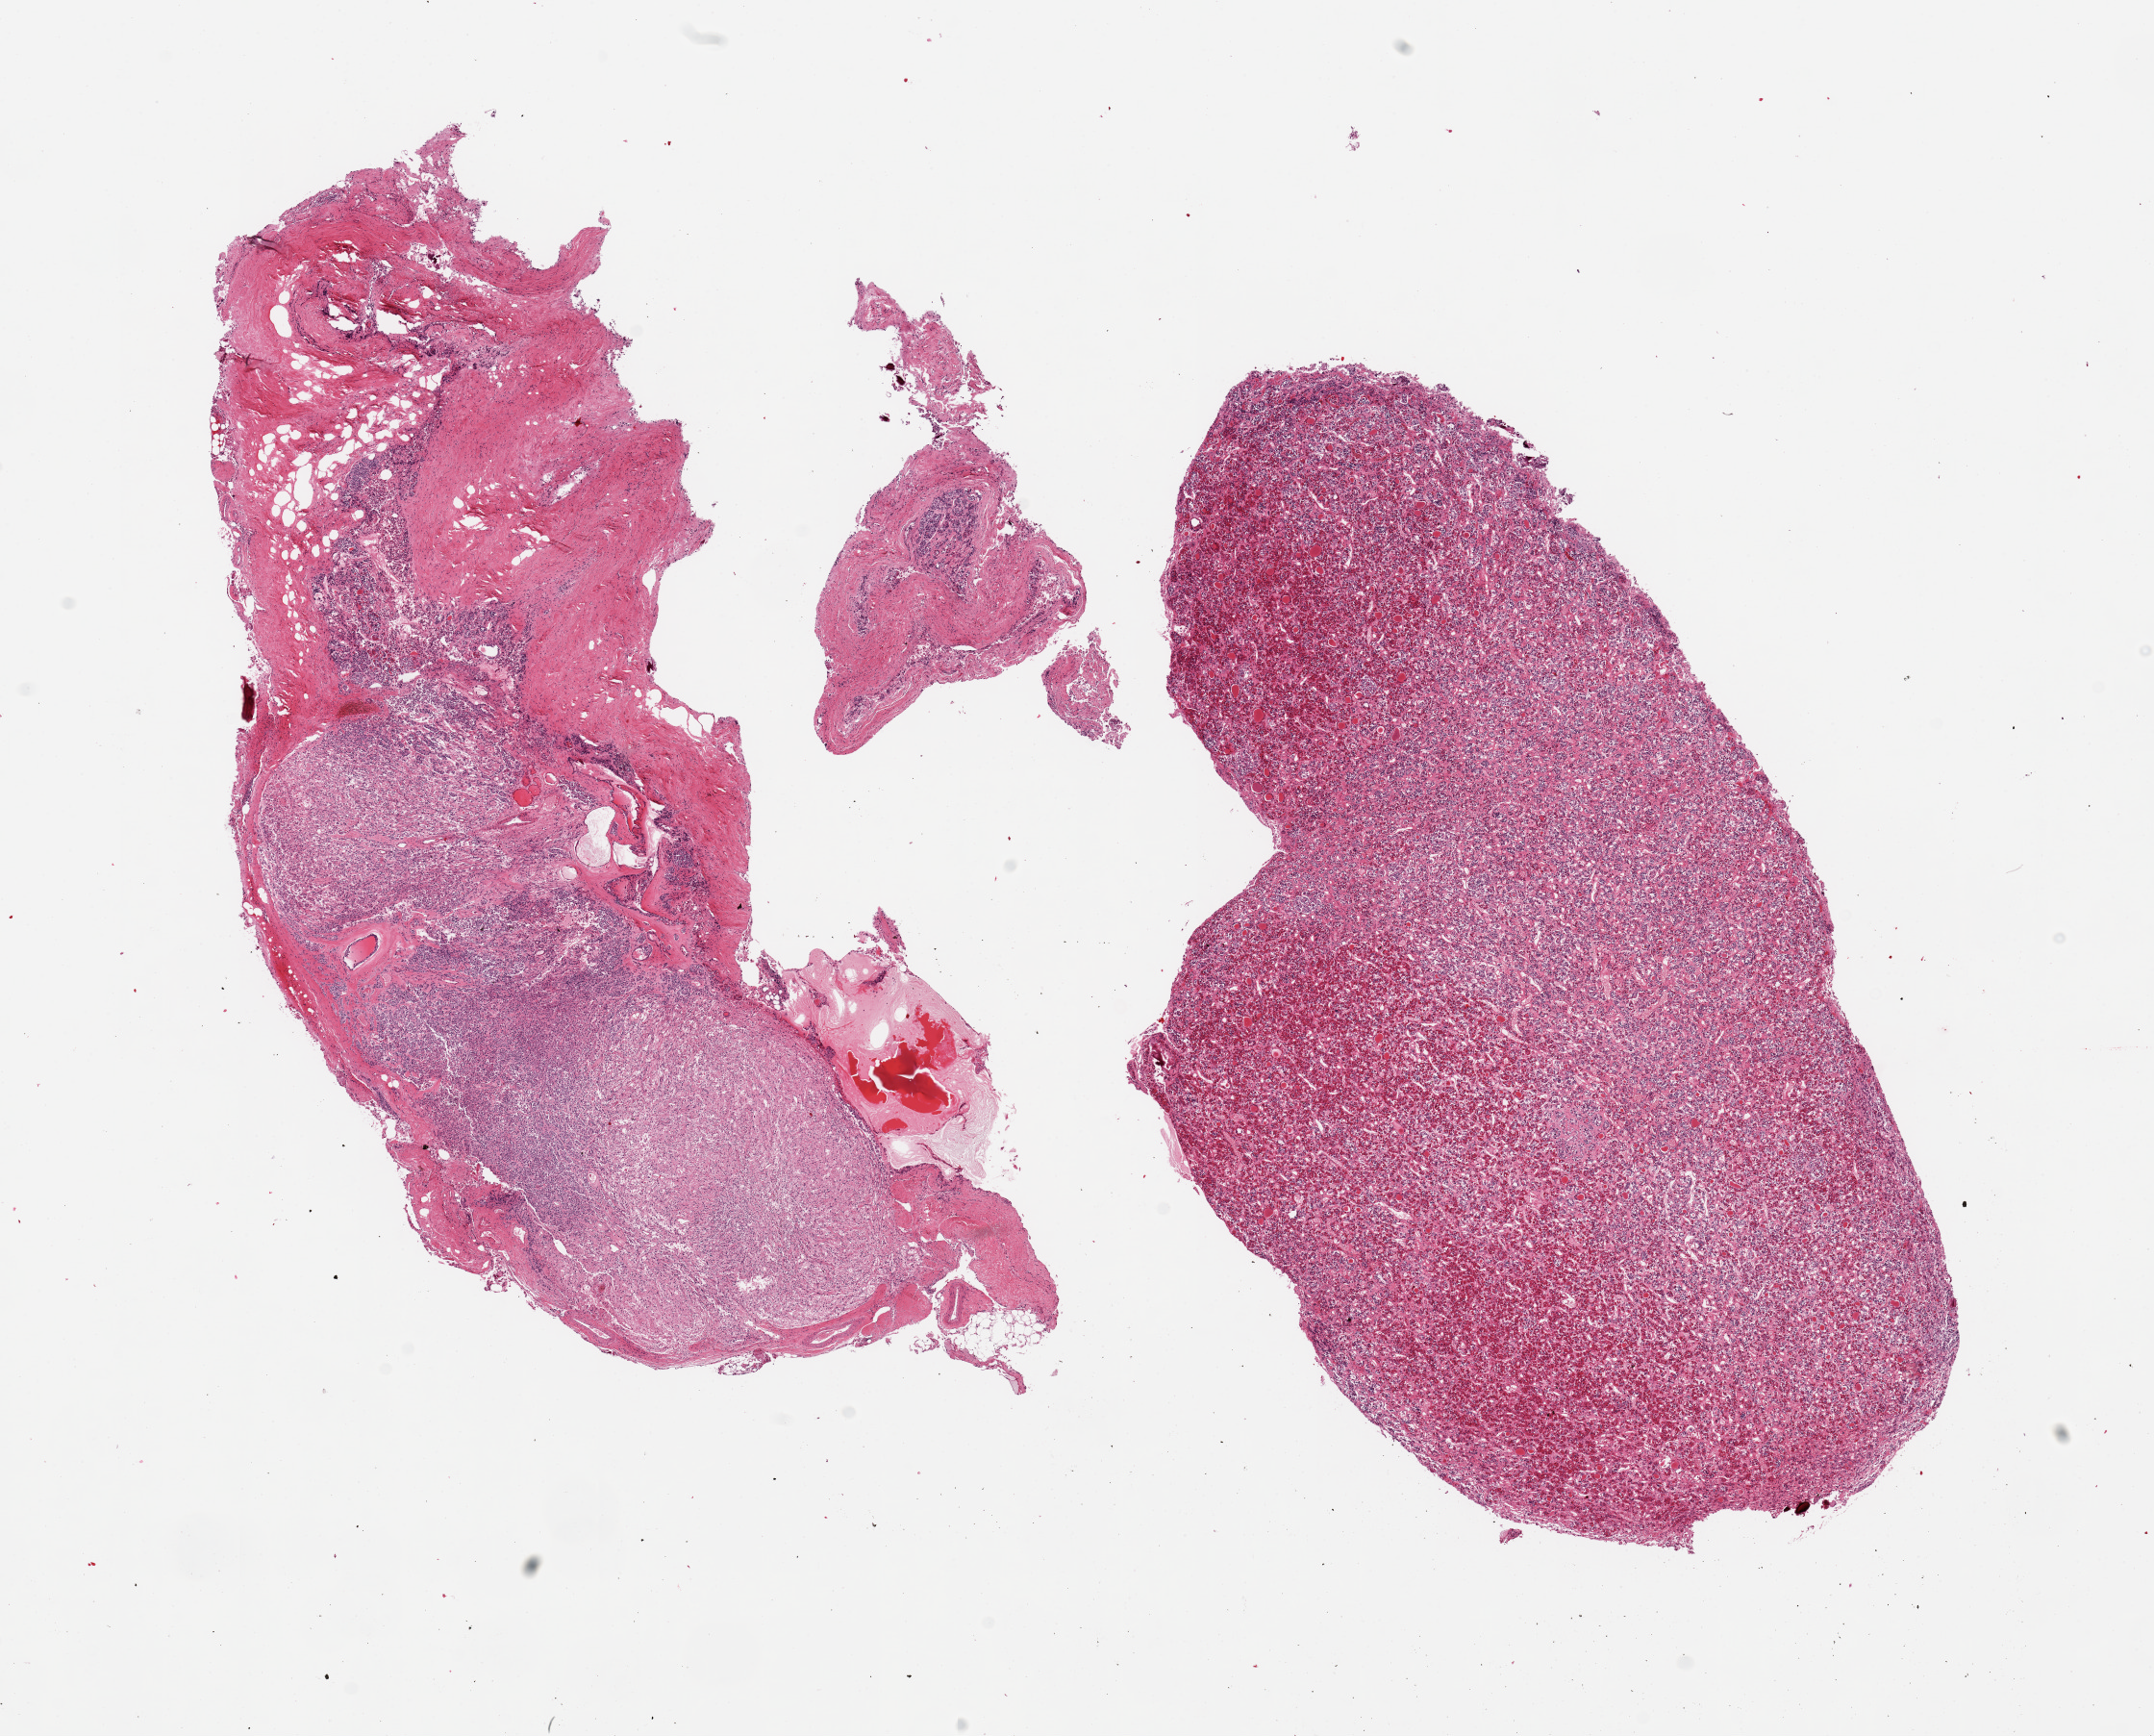
Haematoxylin and eosin whole-slide image, brightfield — whole scanned area (about 17.7 x 14.3 mm, acquisition: 20x scan) shown as a low-resolution overview. PAXgene-fixed, paraffin-embedded tissue. Sampled site (target tissue): pituitary. Tissue donor sample. Female donor.
Reviewer comment on this tissue sample: 2 pieces; neurohypophysis and adenohypophysis and attached bone fragment.